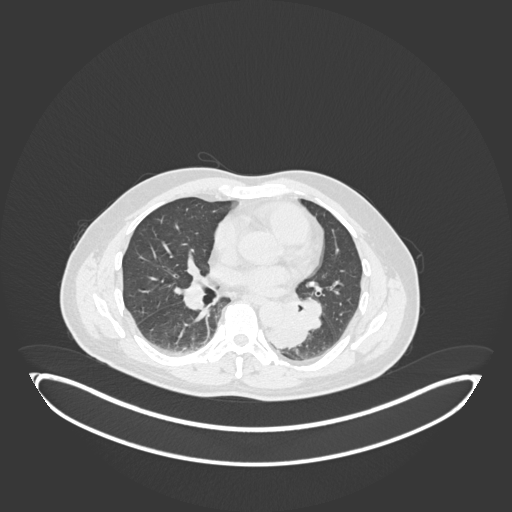
Chest CT, one axial slice; position 96 of 258 along the scan axis; reconstruction kernel B30f; 120 kVp; lung window (W 1500 / L -600 HU); 1 mm slice thickness; 512 × 512 image matrix. Patient: male, 54 years. Case-level facts recorded for this patient, not image findings: clinical TNM (as recorded): T3 N0 M0.
Annotated regions visible in this slice (rectangle marked by the reading radiologist):
- lung tumour (recorded histology: squamous cell carcinoma): box from (x=262, y=303) to (x=311, y=352) px